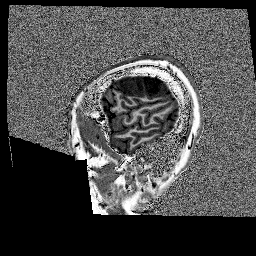
Brain MRI from a brain-tumour surgery series, one sagittal slice. 1 mm slice thickness. 256 × 256 image matrix. From the clinical record (not read from this slice): histopathology: Glioblastoma; WHO grade: 4; IDH mutation: no.
Outlined on this slice (outlined manually by an expert reader):
- tumour: bounding box (x1, y1, x2, y2) in pixels: (118, 75, 175, 97)